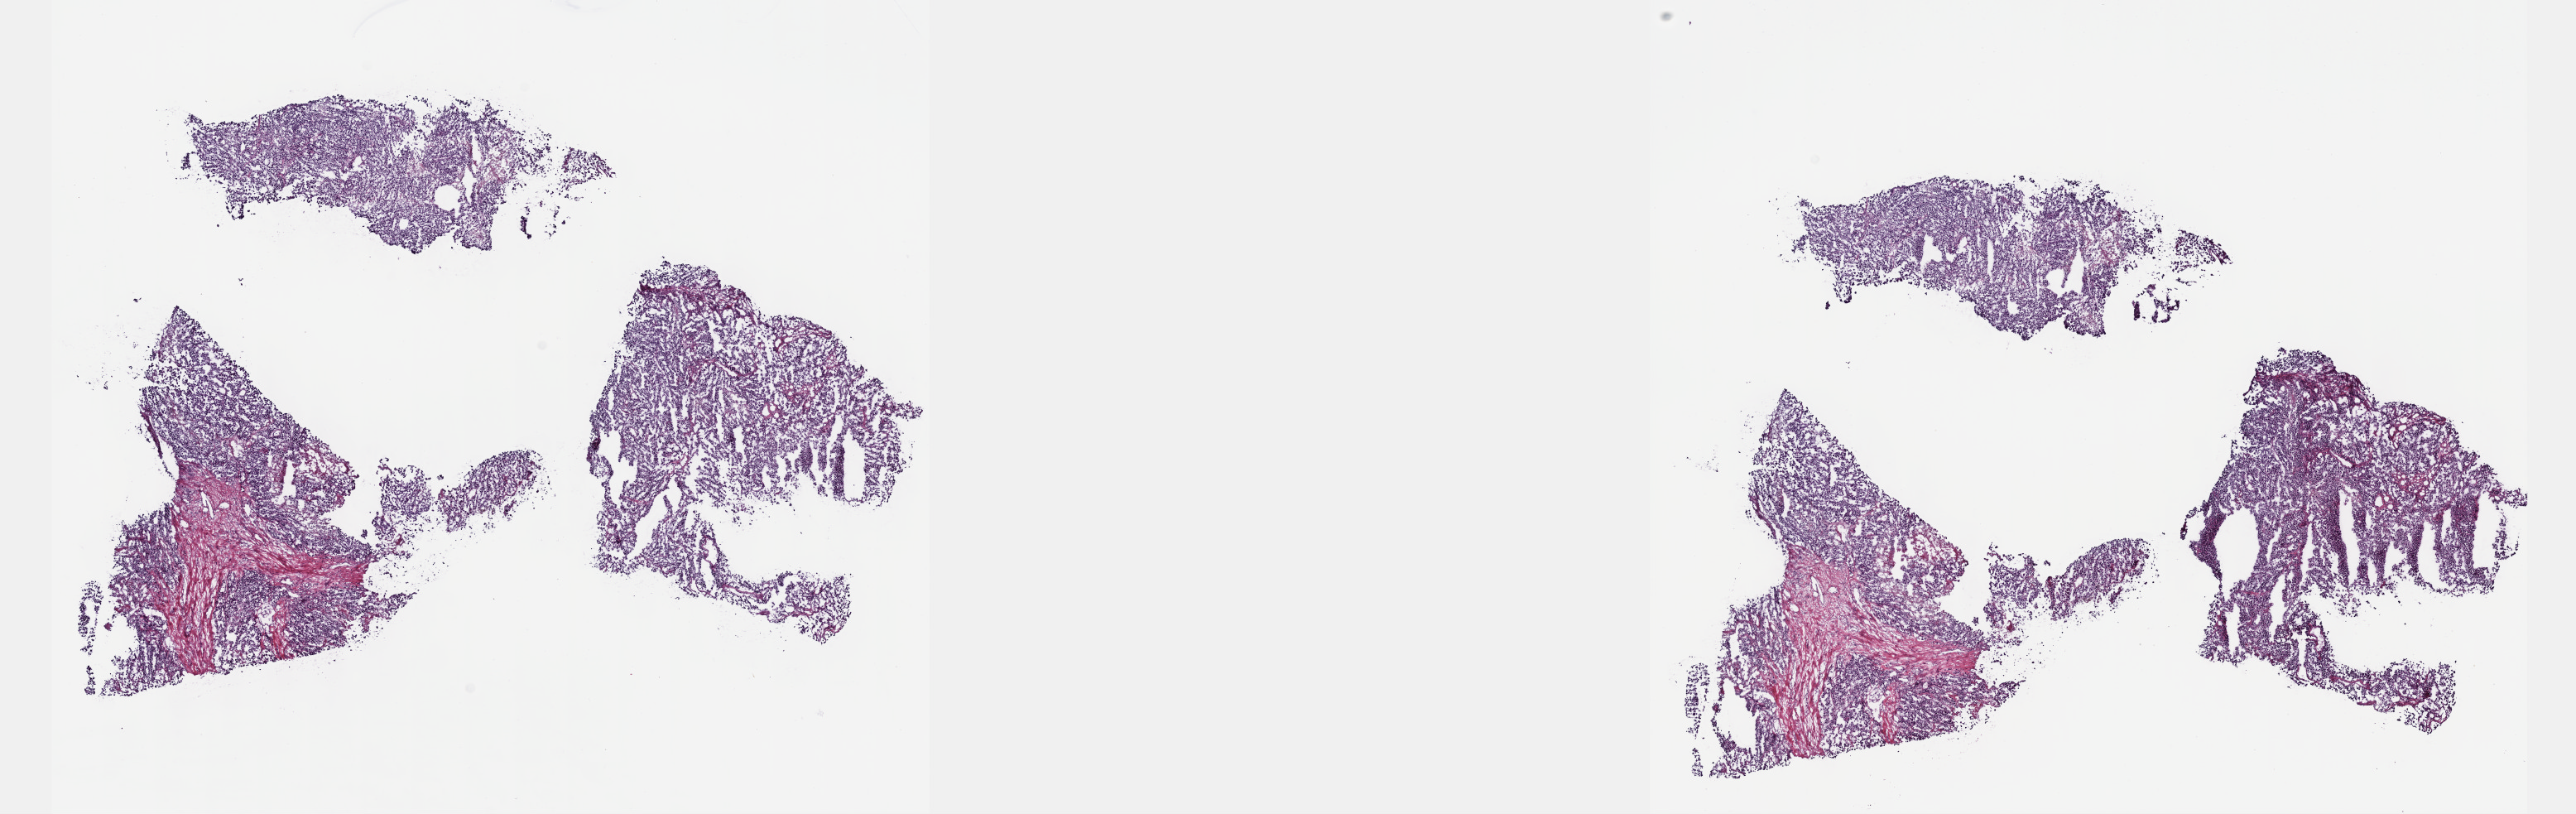
H&E whole-slide image, whole scanned area (about 25.1 x 7.9 mm, acquisition: 40x scan) shown as a low-resolution overview, frozen section from the top of the tissue portion, metastatic tumour sample. Male, age 26 years at initial diagnosis. Composition of this section per pathologist review: tumour cells 80%, tumour nuclei 80%, normal cells 0%, stromal cells 20%, necrosis 0%. Inflammatory infiltration, as recorded: lymphocyte infiltration 3%, monocyte infiltration 1%, neutrophil infiltration 1%.
This section: metastatic tumour tissue. Patient diagnosis: Malignant melanoma, NOS.